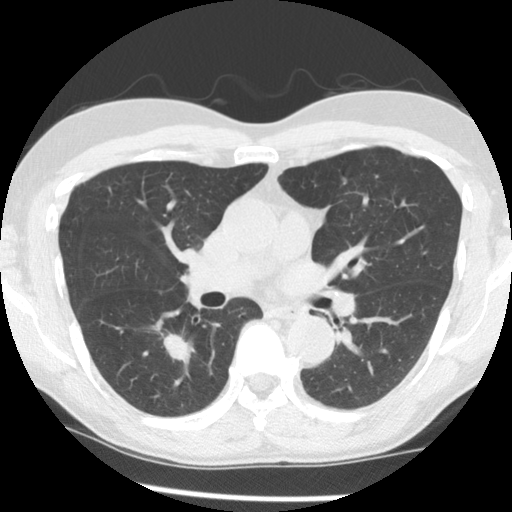
Low-dose screening chest CT, one axial slice; lung window (W 1500 / L -600 HU); 2.5 mm slice thickness; 512 × 512 image matrix, field of view 320 × 320 mm.
Outlined on this slice (expert manual segmentation):
- lesion 1 (tumor, lower lobe of right lung): bounding box (x1, y1, x2, y2) in pixels: (163, 333, 188, 360)